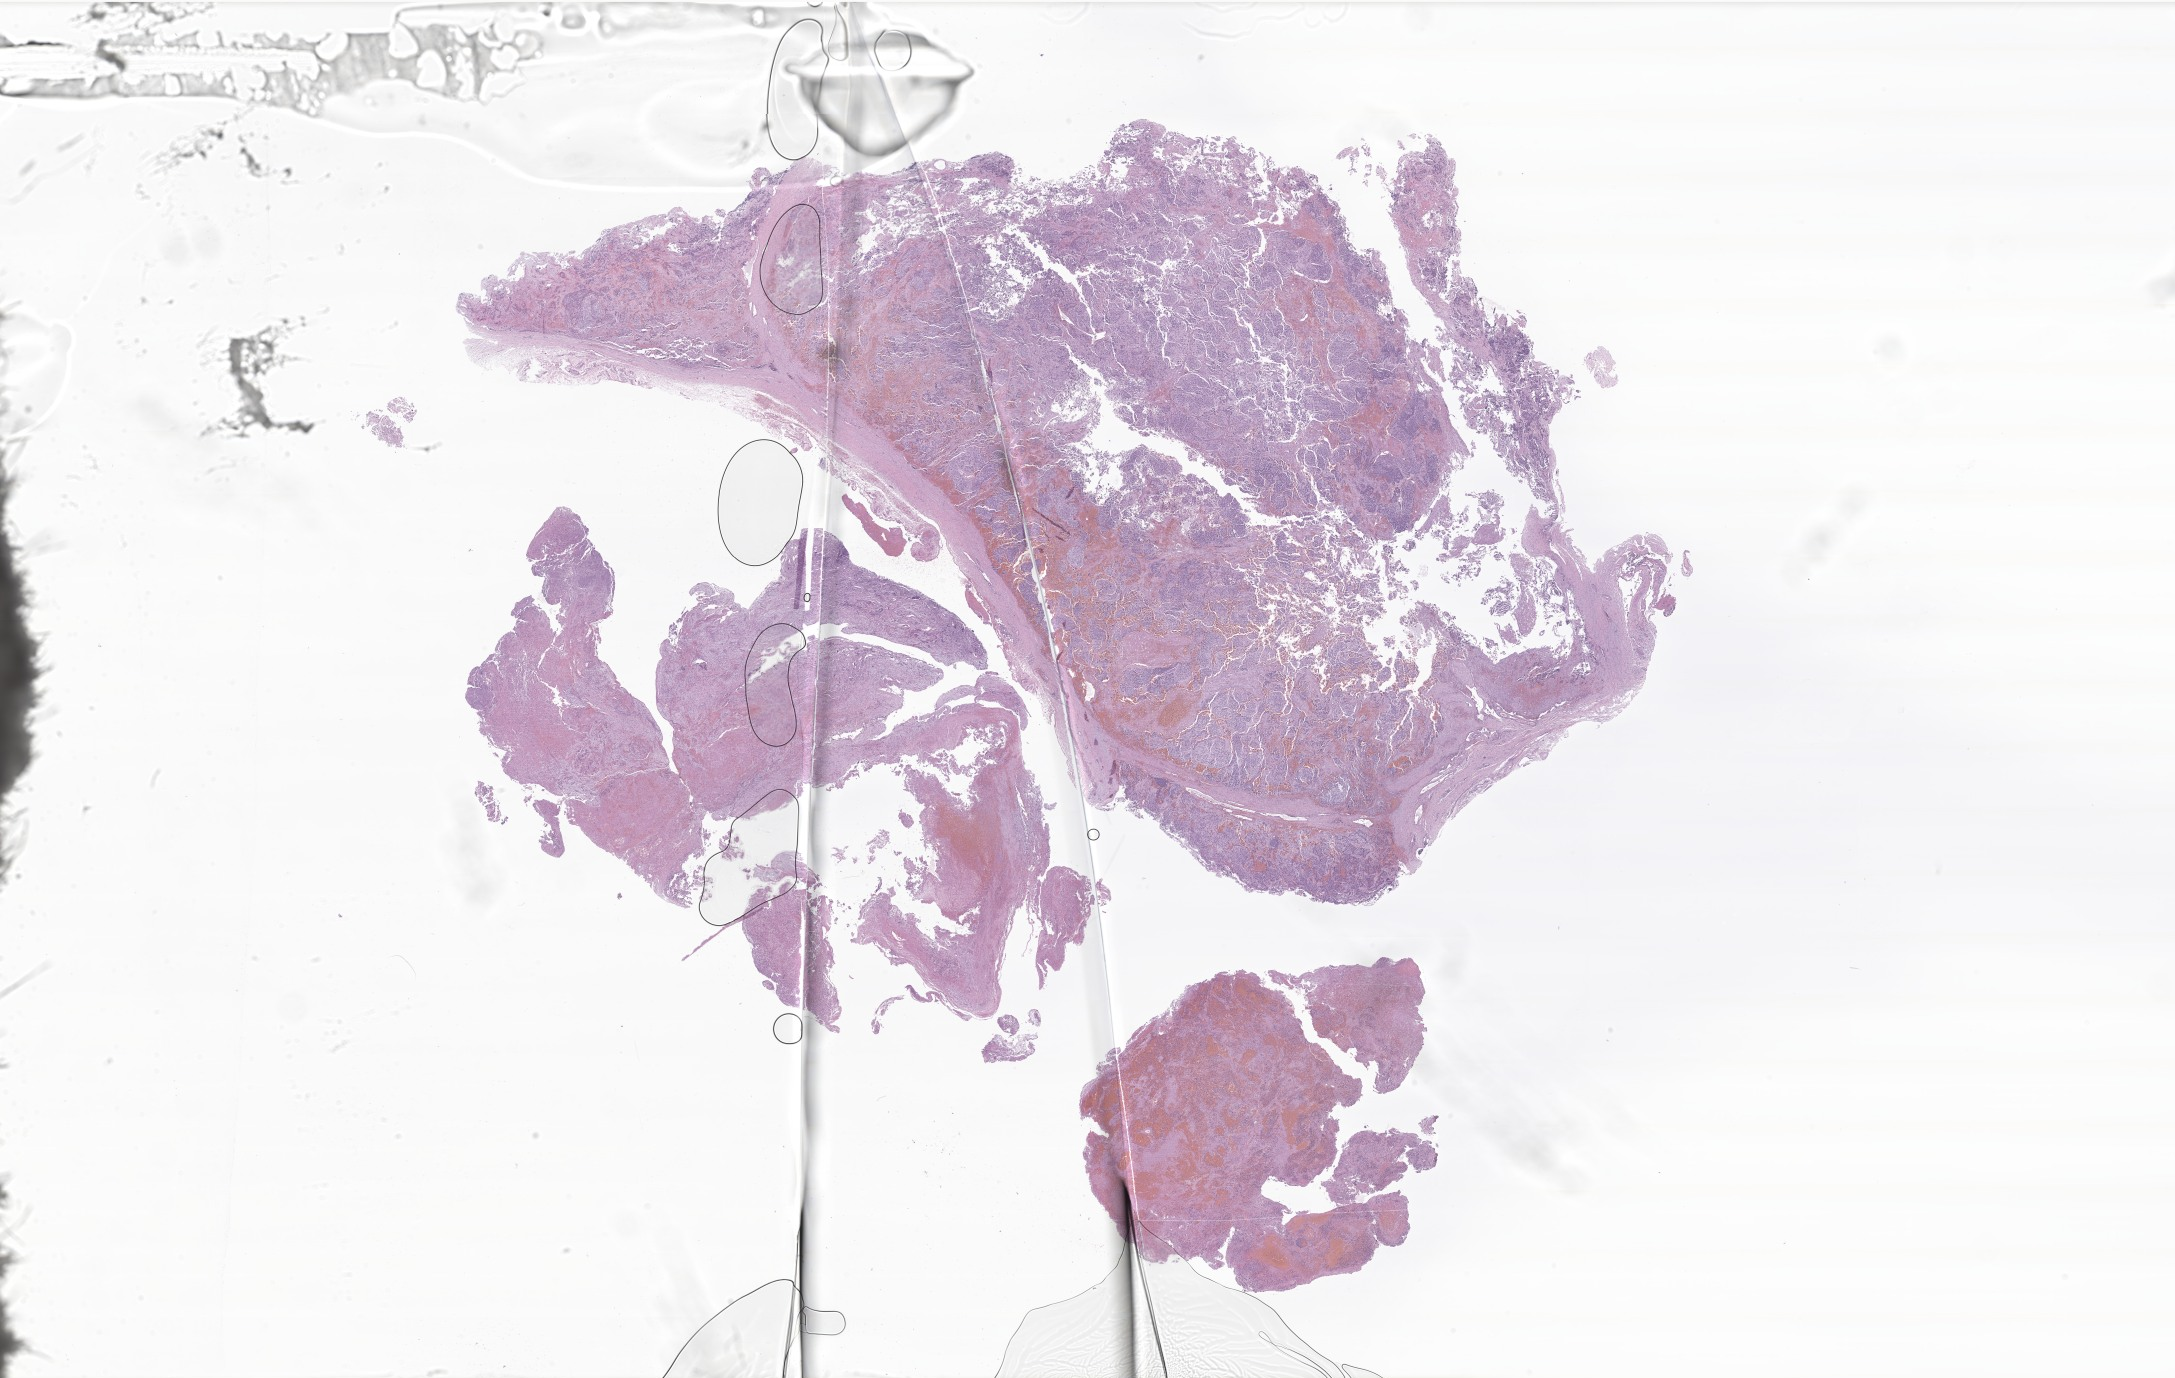
H&E whole-slide image of tumor tissue from the retroperitoneum — a low-resolution overview of the entire scanned area, about 36.7 x 23.2 mm; formalin-fixed paraffin-embedded section. Patient: male, age 37 months (3 years 1 month).
Recorded diagnosis: Neuroblastoma, NOS.